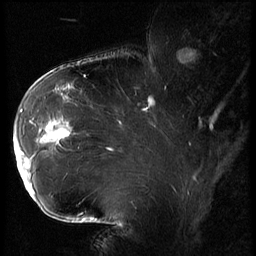
Breast MRI (dynamic contrast-enhanced), one sagittal slice. Slice 42 of 62 in the series (ordered by position). 3 images stored at this slice position (order not interpretable as contrast timing). 1.5 T. TE 4.2 ms, TR 9 ms. 2.5 mm slice thickness. 256 × 256 image matrix. Female patient, age 43 years. From the clinical record (not read from this slice): setting: breast cancer imaged before/during neoadjuvant chemotherapy; receptor status: HER2-positive.
Outlined on this slice (semi-automatically segmented with operator editing):
- analysis volume of interest (the breast-tissue region the enhancement analysis was run in; not a lesion): bounding box [x1, y1, x2, y2] px = [14, 90, 82, 203]
- tumour enhancement mask (voxels above the 140 % enhancement threshold inside the analysis volume of interest): [14, 96, 73, 195]